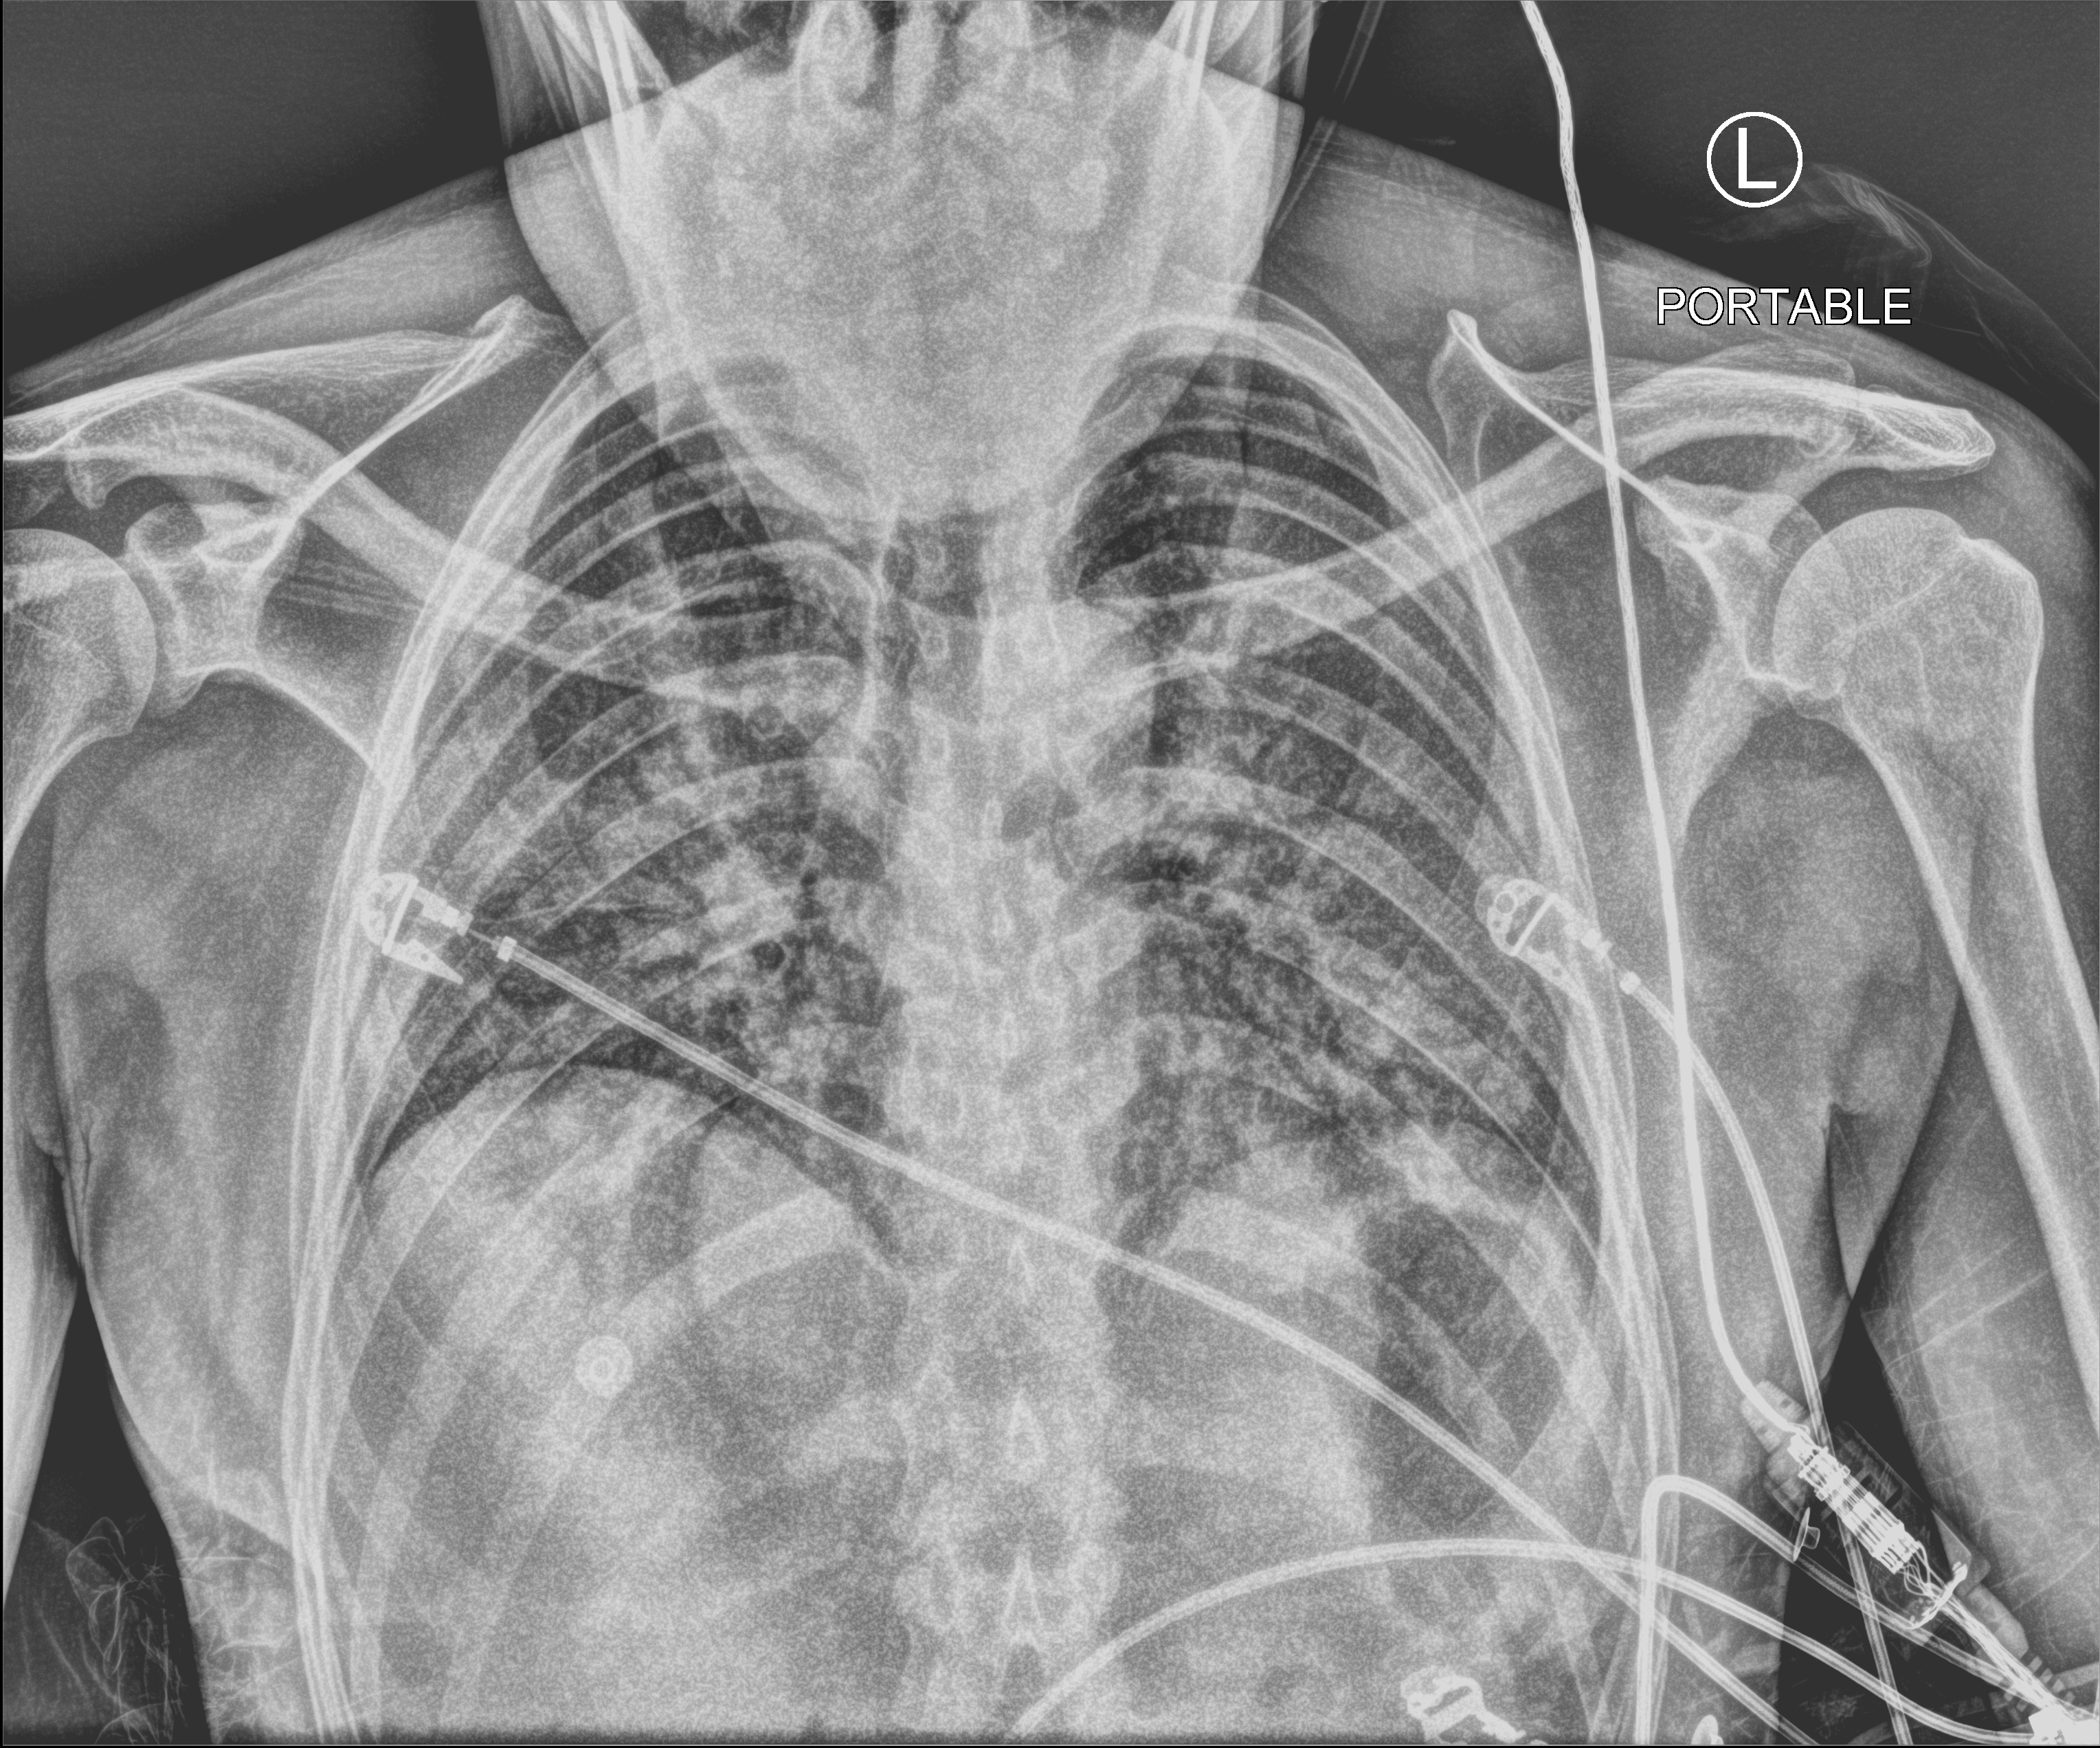
Bedside chest radiograph (computed radiography); anteroposterior (AP) projection. Male patient hospitalised with COVID-19, age 18–59 years.
From the hospital-stay record, not from the radiograph (when in the stay this image was taken is not recorded):
- diabetes (admission record): no
- admitted to intensive care during this hospital stay: yes
- mechanically ventilated during this hospital stay: no